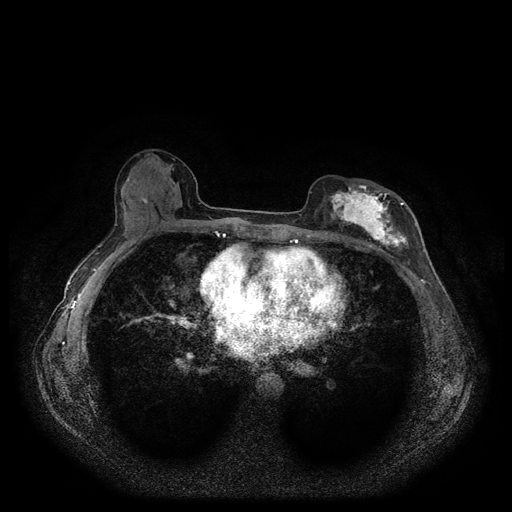
Breast MRI (dynamic contrast-enhanced, multi-phase), one axial slice; slice 53 of 116 in the series (ordered by position); dynamic contrast-enhanced series, time point 2 of 5 at this slice position (early post-contrast); 1.5 T; TE 2.6 ms, TR 5.3 ms; 2 mm slice thickness; 512 × 512 image matrix, field of view 350 × 350 mm. Patient: female, 51 years.
Structures marked on this image (semi-automatically segmented with operator editing):
- breast lesion (labelled 'tumour' in the annotation; benign lesions carry a separate 'benign' label): bounding box <324,186,414,252> (left, top, right, bottom; pixels)